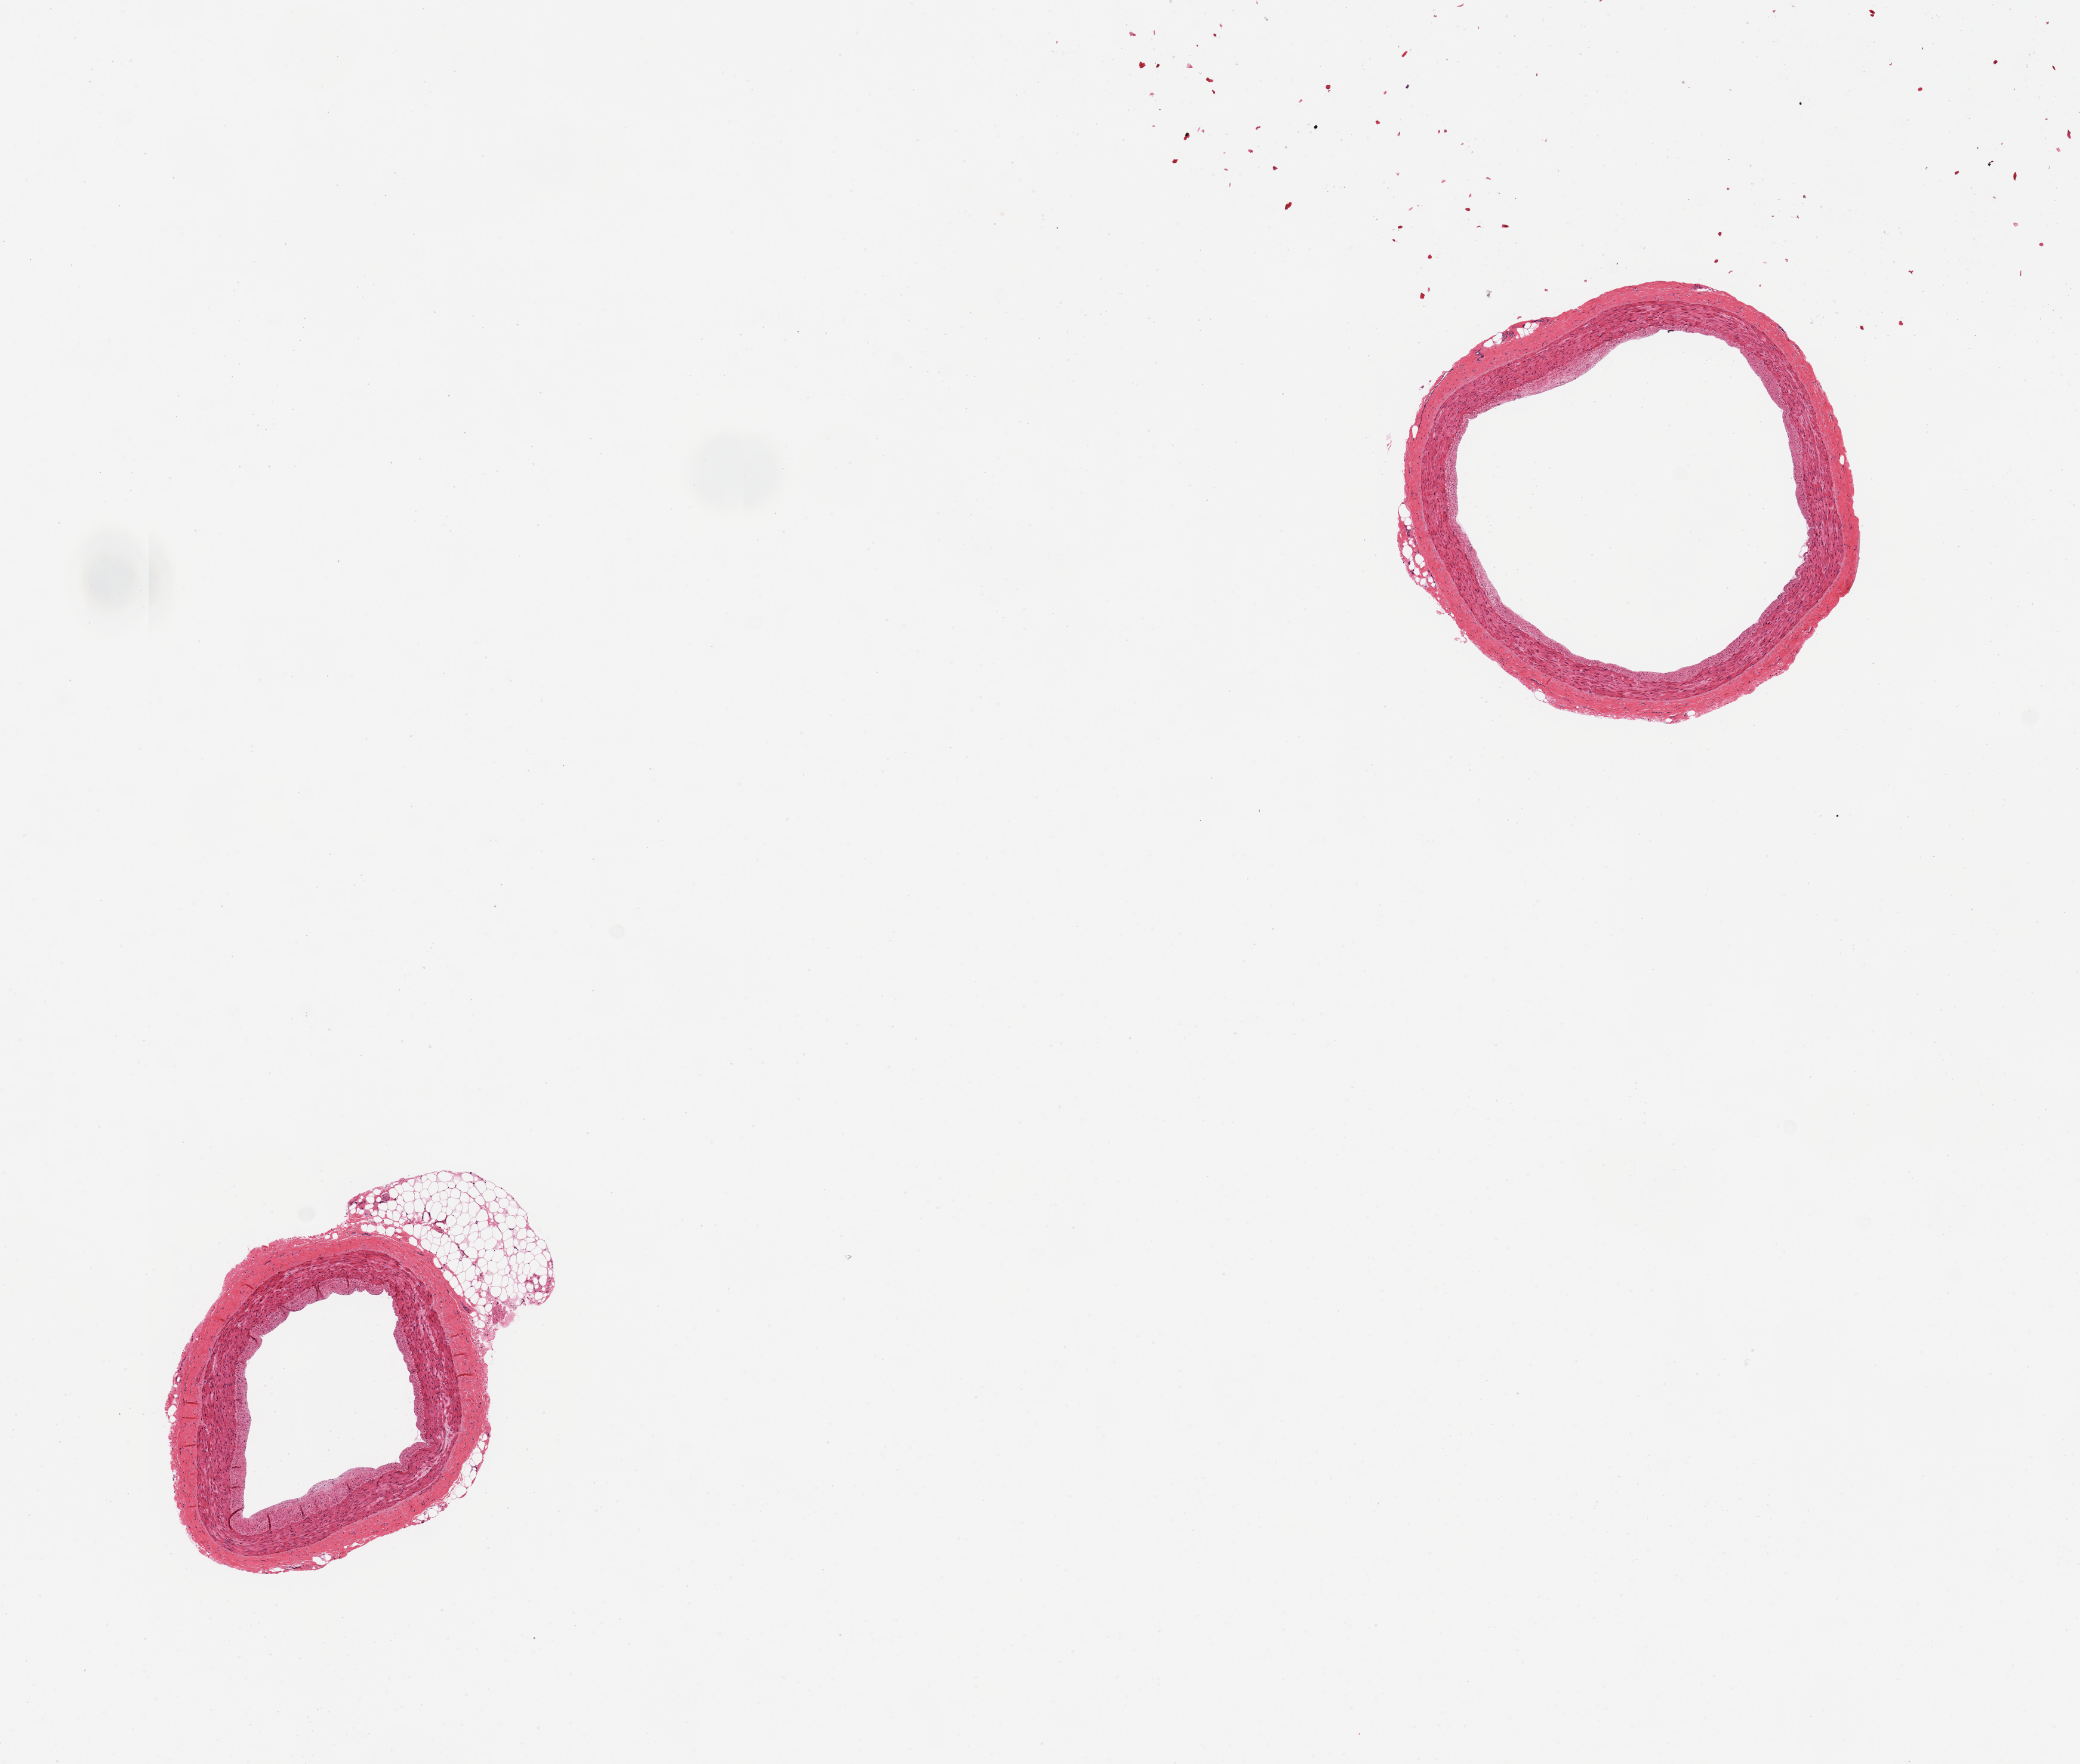
Whole-slide image, haematoxylin and eosin stain — a low-resolution overview of the entire scanned area, about 13.8 x 11.7 mm, PAXgene-fixed, paraffin-embedded tissue, target tissue: coronary artery, donor tissue sample. Female donor.
* review note (as recorded): 2 pieces, minute (~0.5mm nubbin) ahderent fat; no visible atherosis